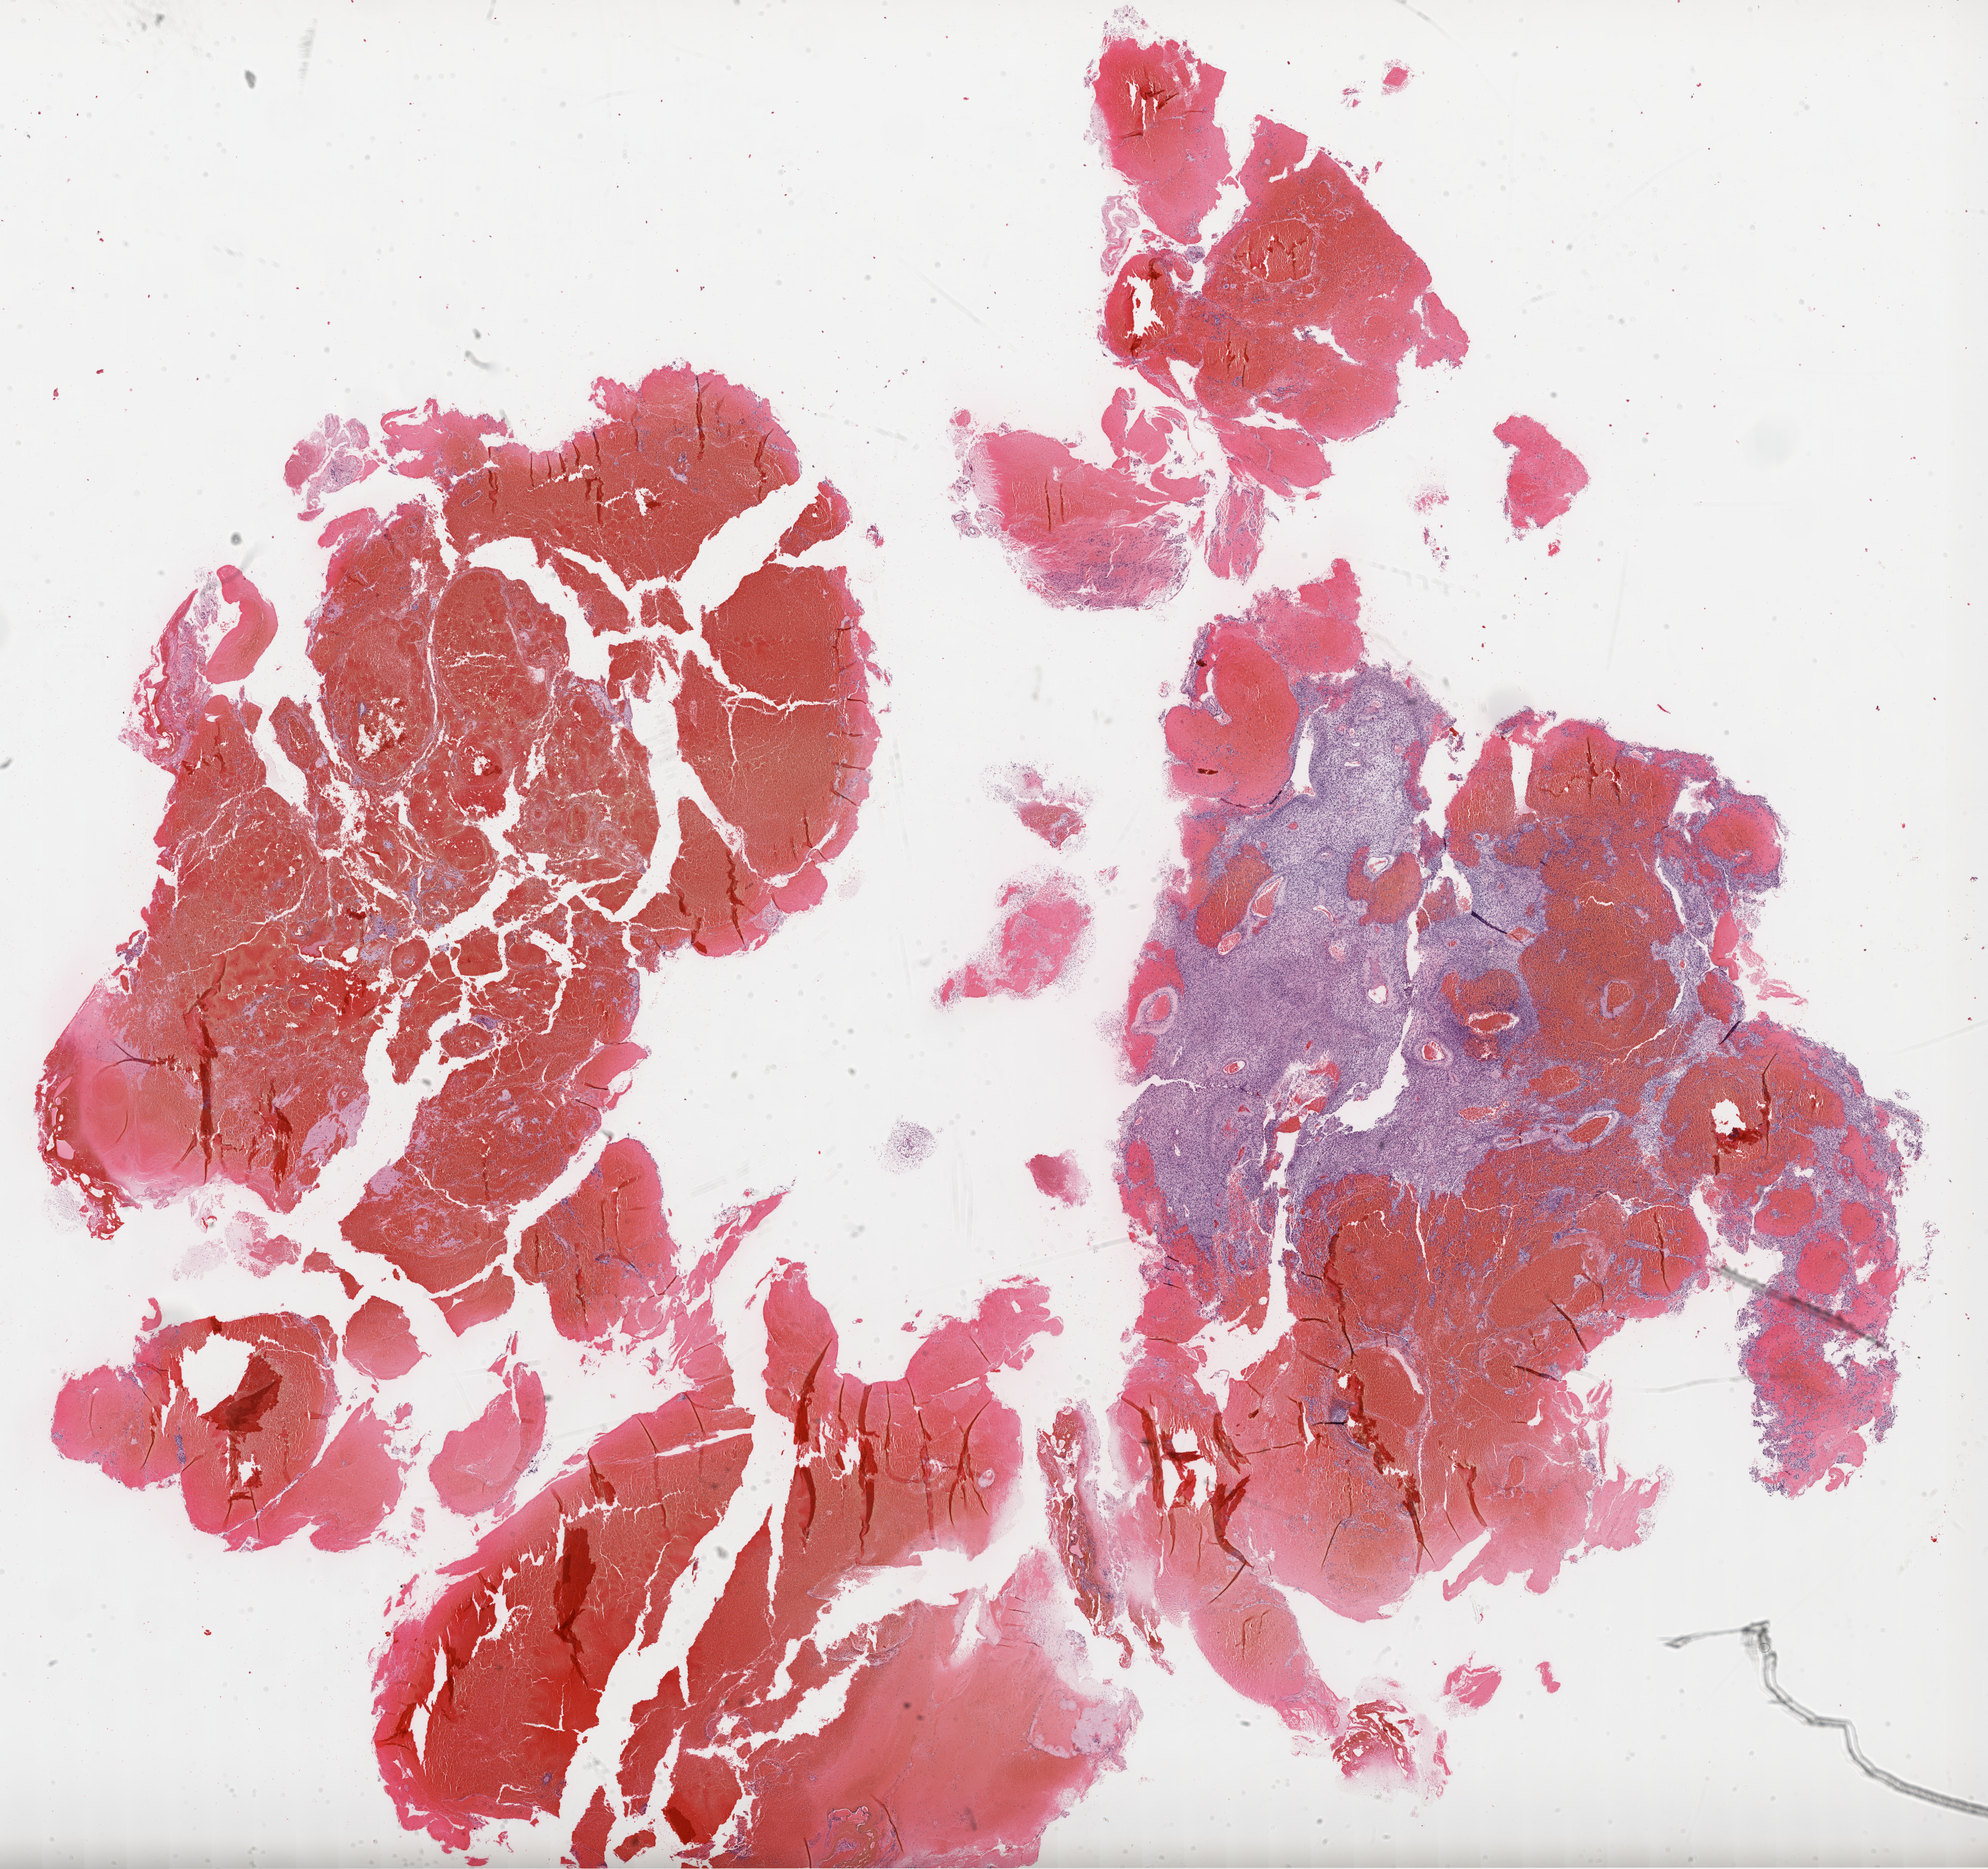
Digitized H&E-stained tissue section (whole slide) — low-resolution overview of the scanned area, about 22.7 x 21.4 mm (acquisition: 20x scan), formalin-fixed paraffin-embedded (FFPE) diagnostic section, brain, primary tumour sample. Male patient; age at initial diagnosis 54 years.
Histologic diagnosis: Glioblastoma.